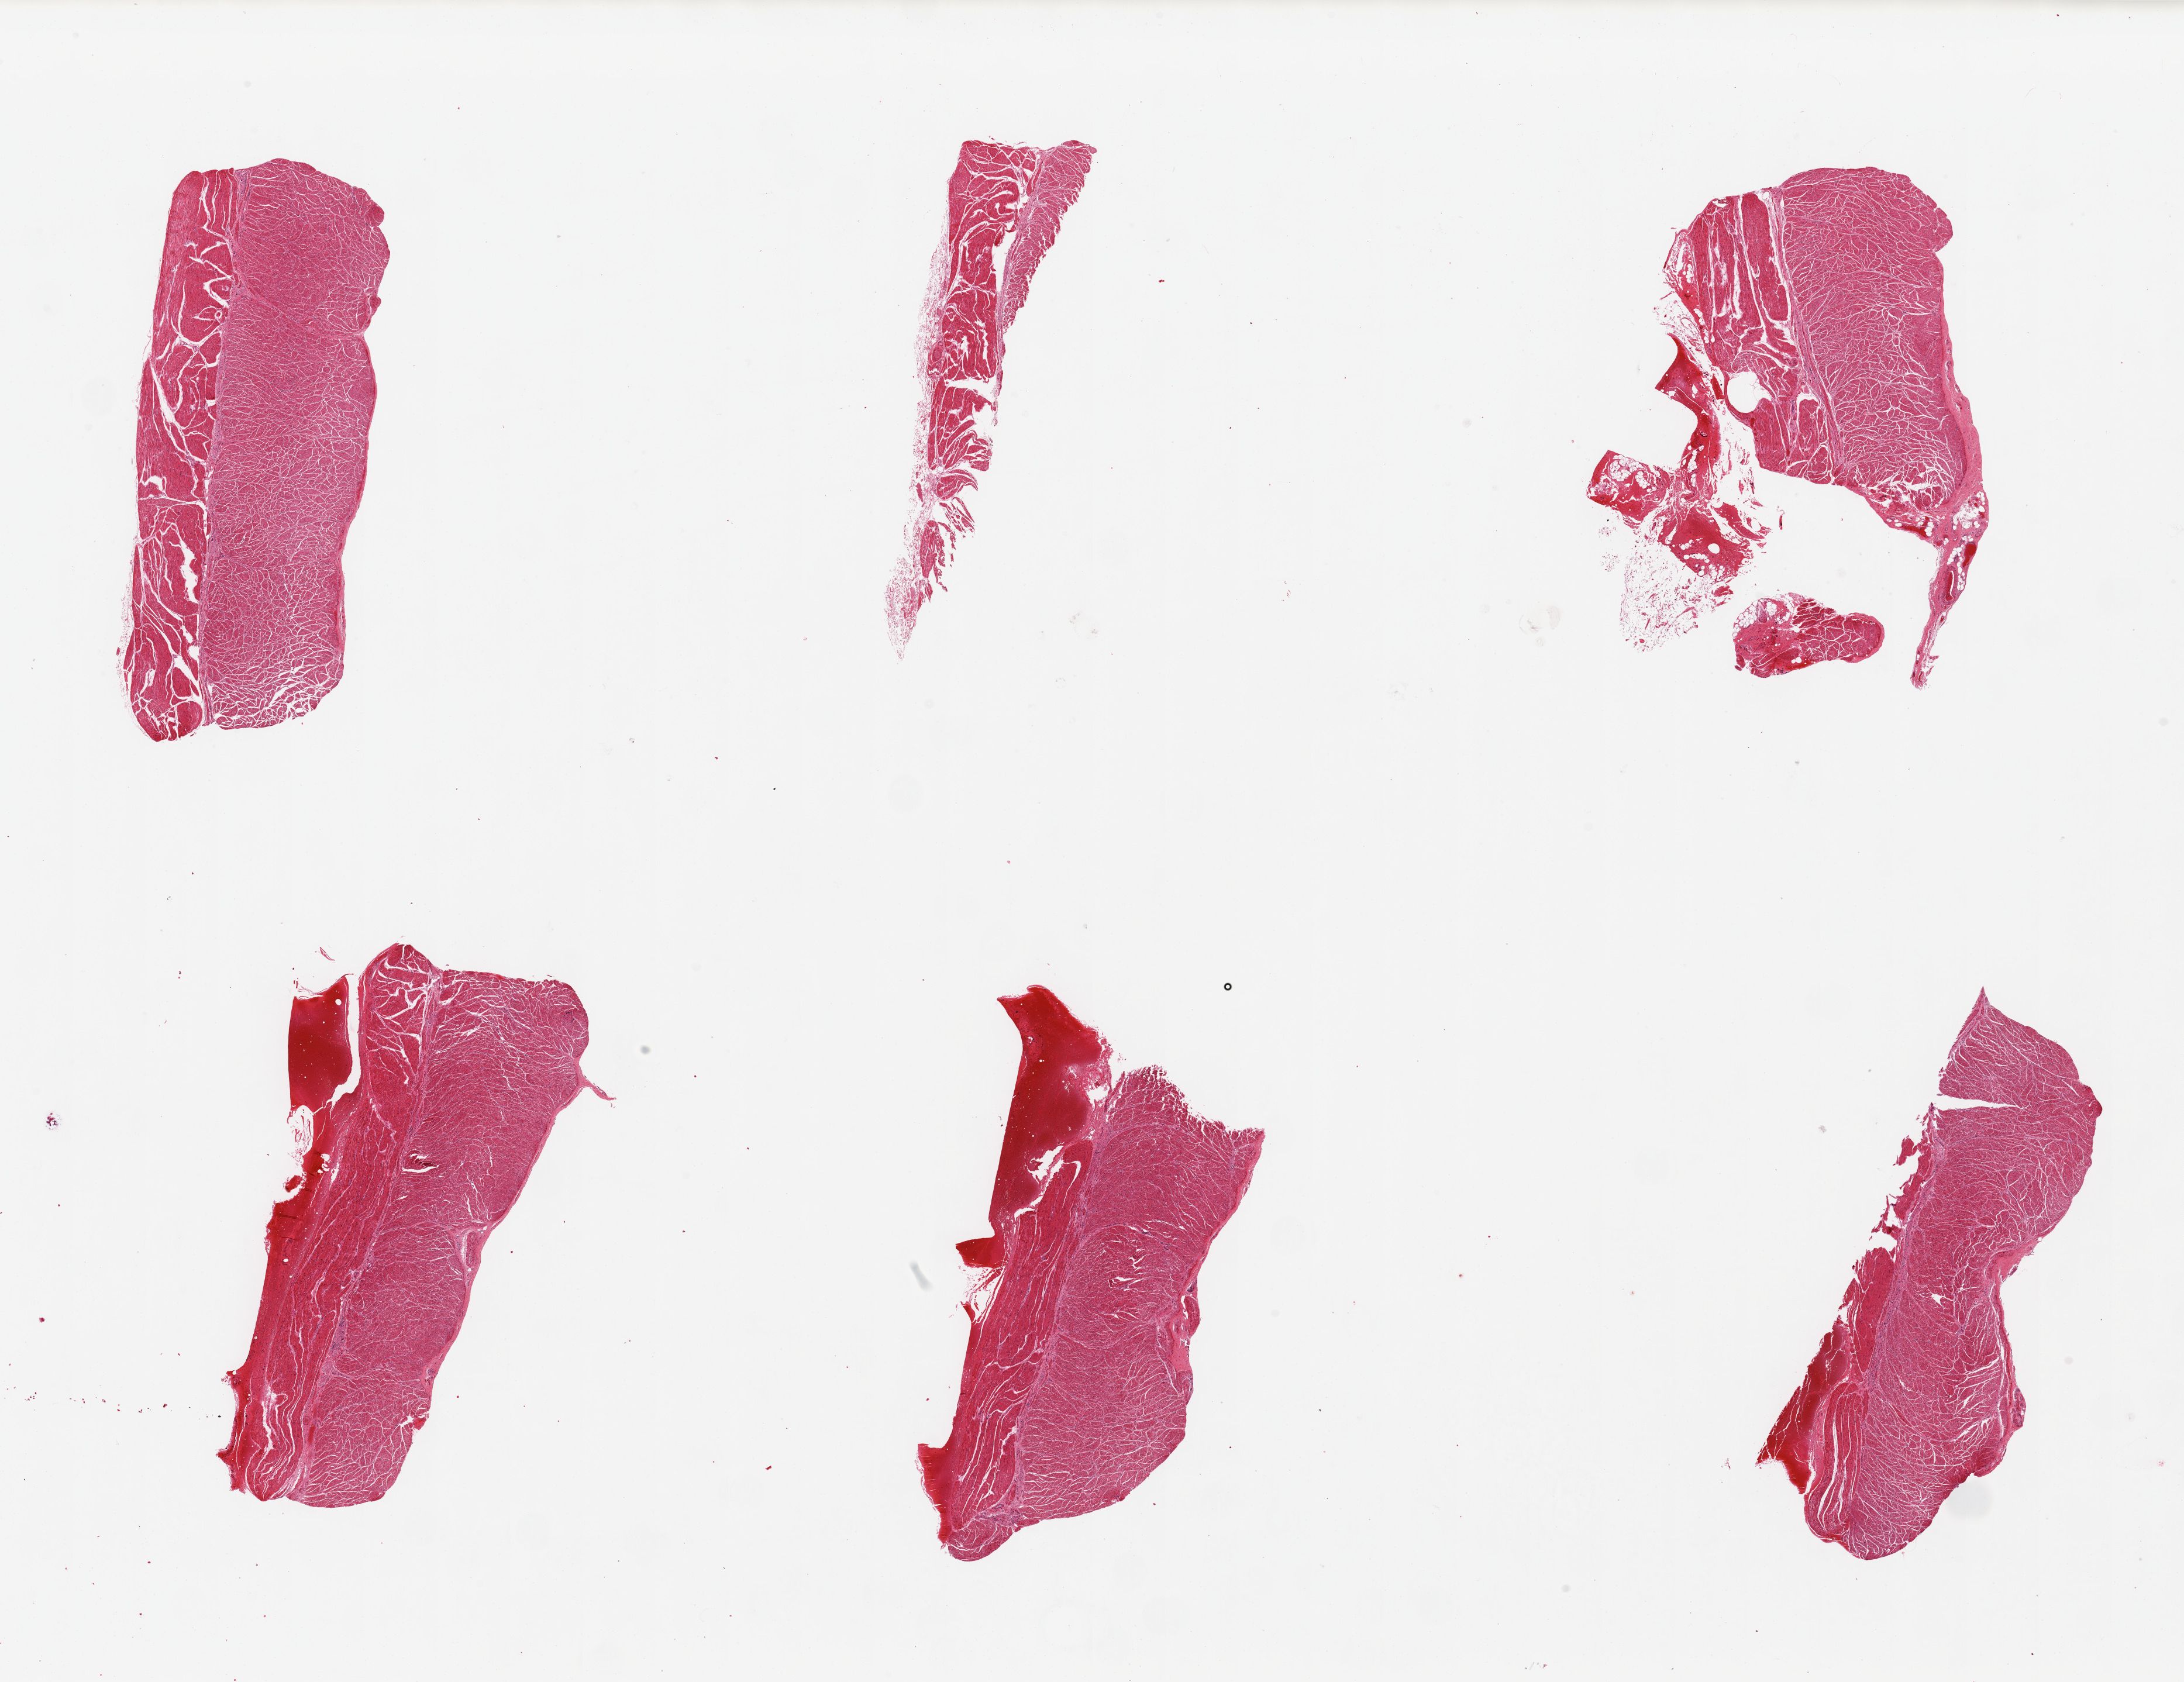
Digitized H&E-stained section, brightfield, shown as a low-resolution overview of the whole scanned area (about 29.5 x 22.7 mm, acquisition: 20x scan); PAXgene-fixed, paraffin-embedded tissue; target tissue: esophageal muscle; donor tissue sample. Donor sex: male.
Pathologist's review note for this sample: 6 pieces ~7x3mm.